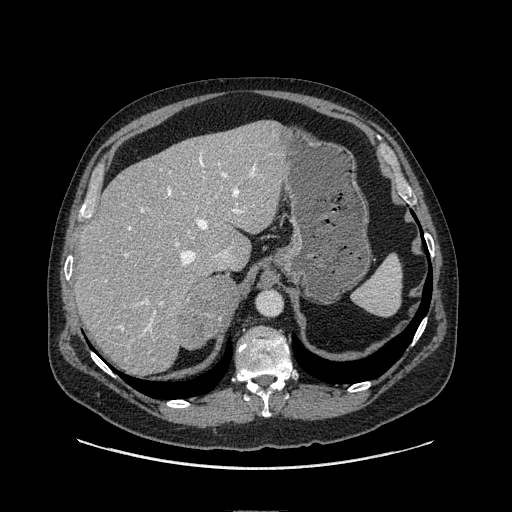
Contrast-enhanced abdominal CT, one axial slice; position 81 of 149 along the scan axis; soft-tissue window (W 400 / L 40 HU); 1.25 mm slice thickness; 512 × 512 image matrix. Male patient. Case-level facts recorded for this patient, not image findings: diagnosis: adrenocortical carcinoma; tumour side: right adrenal.
Structures marked on this image (semi-automatic segmentation, software-assisted and operator-edited):
- mass: bounding box <183,275,238,347> (left, top, right, bottom; pixels)